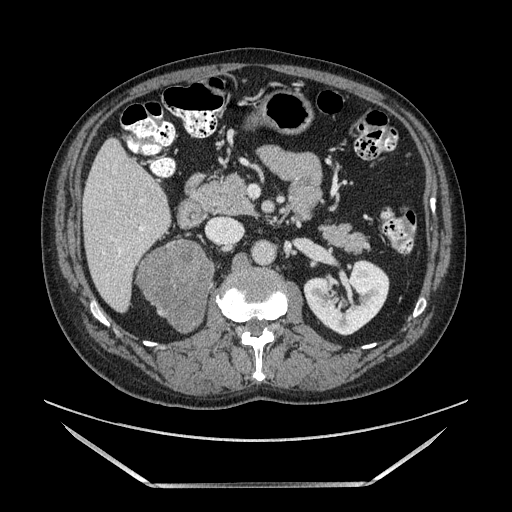
Contrast-enhanced abdominal CT, one axial slice. Slice 59 of 185 in the series (ordered by position). Soft-tissue window (W 400 / L 40 HU). 512 × 512 image matrix, field of view 440 × 440 mm. Male patient. From the clinical record (not read from this slice): diagnosis: adrenocortical carcinoma; tumour side: right adrenal; tumour size at pathology: 10.3 cm; Ki-67 index: 20 %.
Outlined on this slice (semi-automatic segmentation, software-assisted and operator-edited):
- mass: bounding box (x1, y1, x2, y2) in pixels: (135, 245, 210, 332)